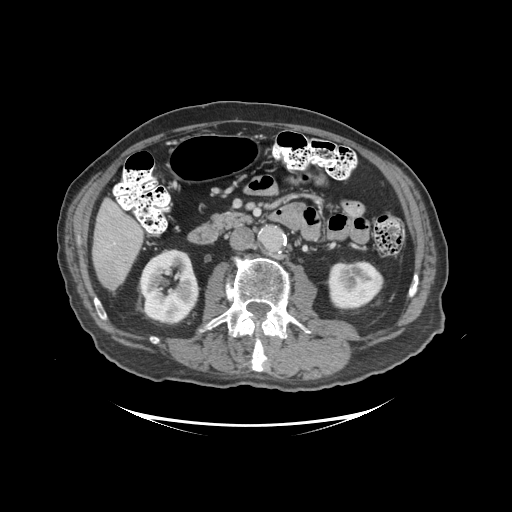
Contrast-enhanced abdominal CT (liver protocol), one axial slice; slice 34 of 99 in the series (ordered by position); reconstruction kernel STANDARD; soft-tissue window (W 400 / L 40 HU); 2.5 mm slice thickness; 512 × 512 image matrix. From the clinical record (not read from this slice): diagnosis: hepatocellular carcinoma (patient treated with transarterial chemoembolisation; whether this scan precedes or follows treatment is not stated here); TNM stage (as recorded): Stage-I; Child-Pugh class: A; tumour differentiation: moderately differentiated.
Annotated regions visible in this slice (semi-automatic segmentation, software-assisted and operator-edited):
- liver parenchyma outside the tumour (the mass and vessels are separate outlines, so this box may not span the whole liver): bounding box [x1, y1, x2, y2] px = [92, 198, 142, 290]